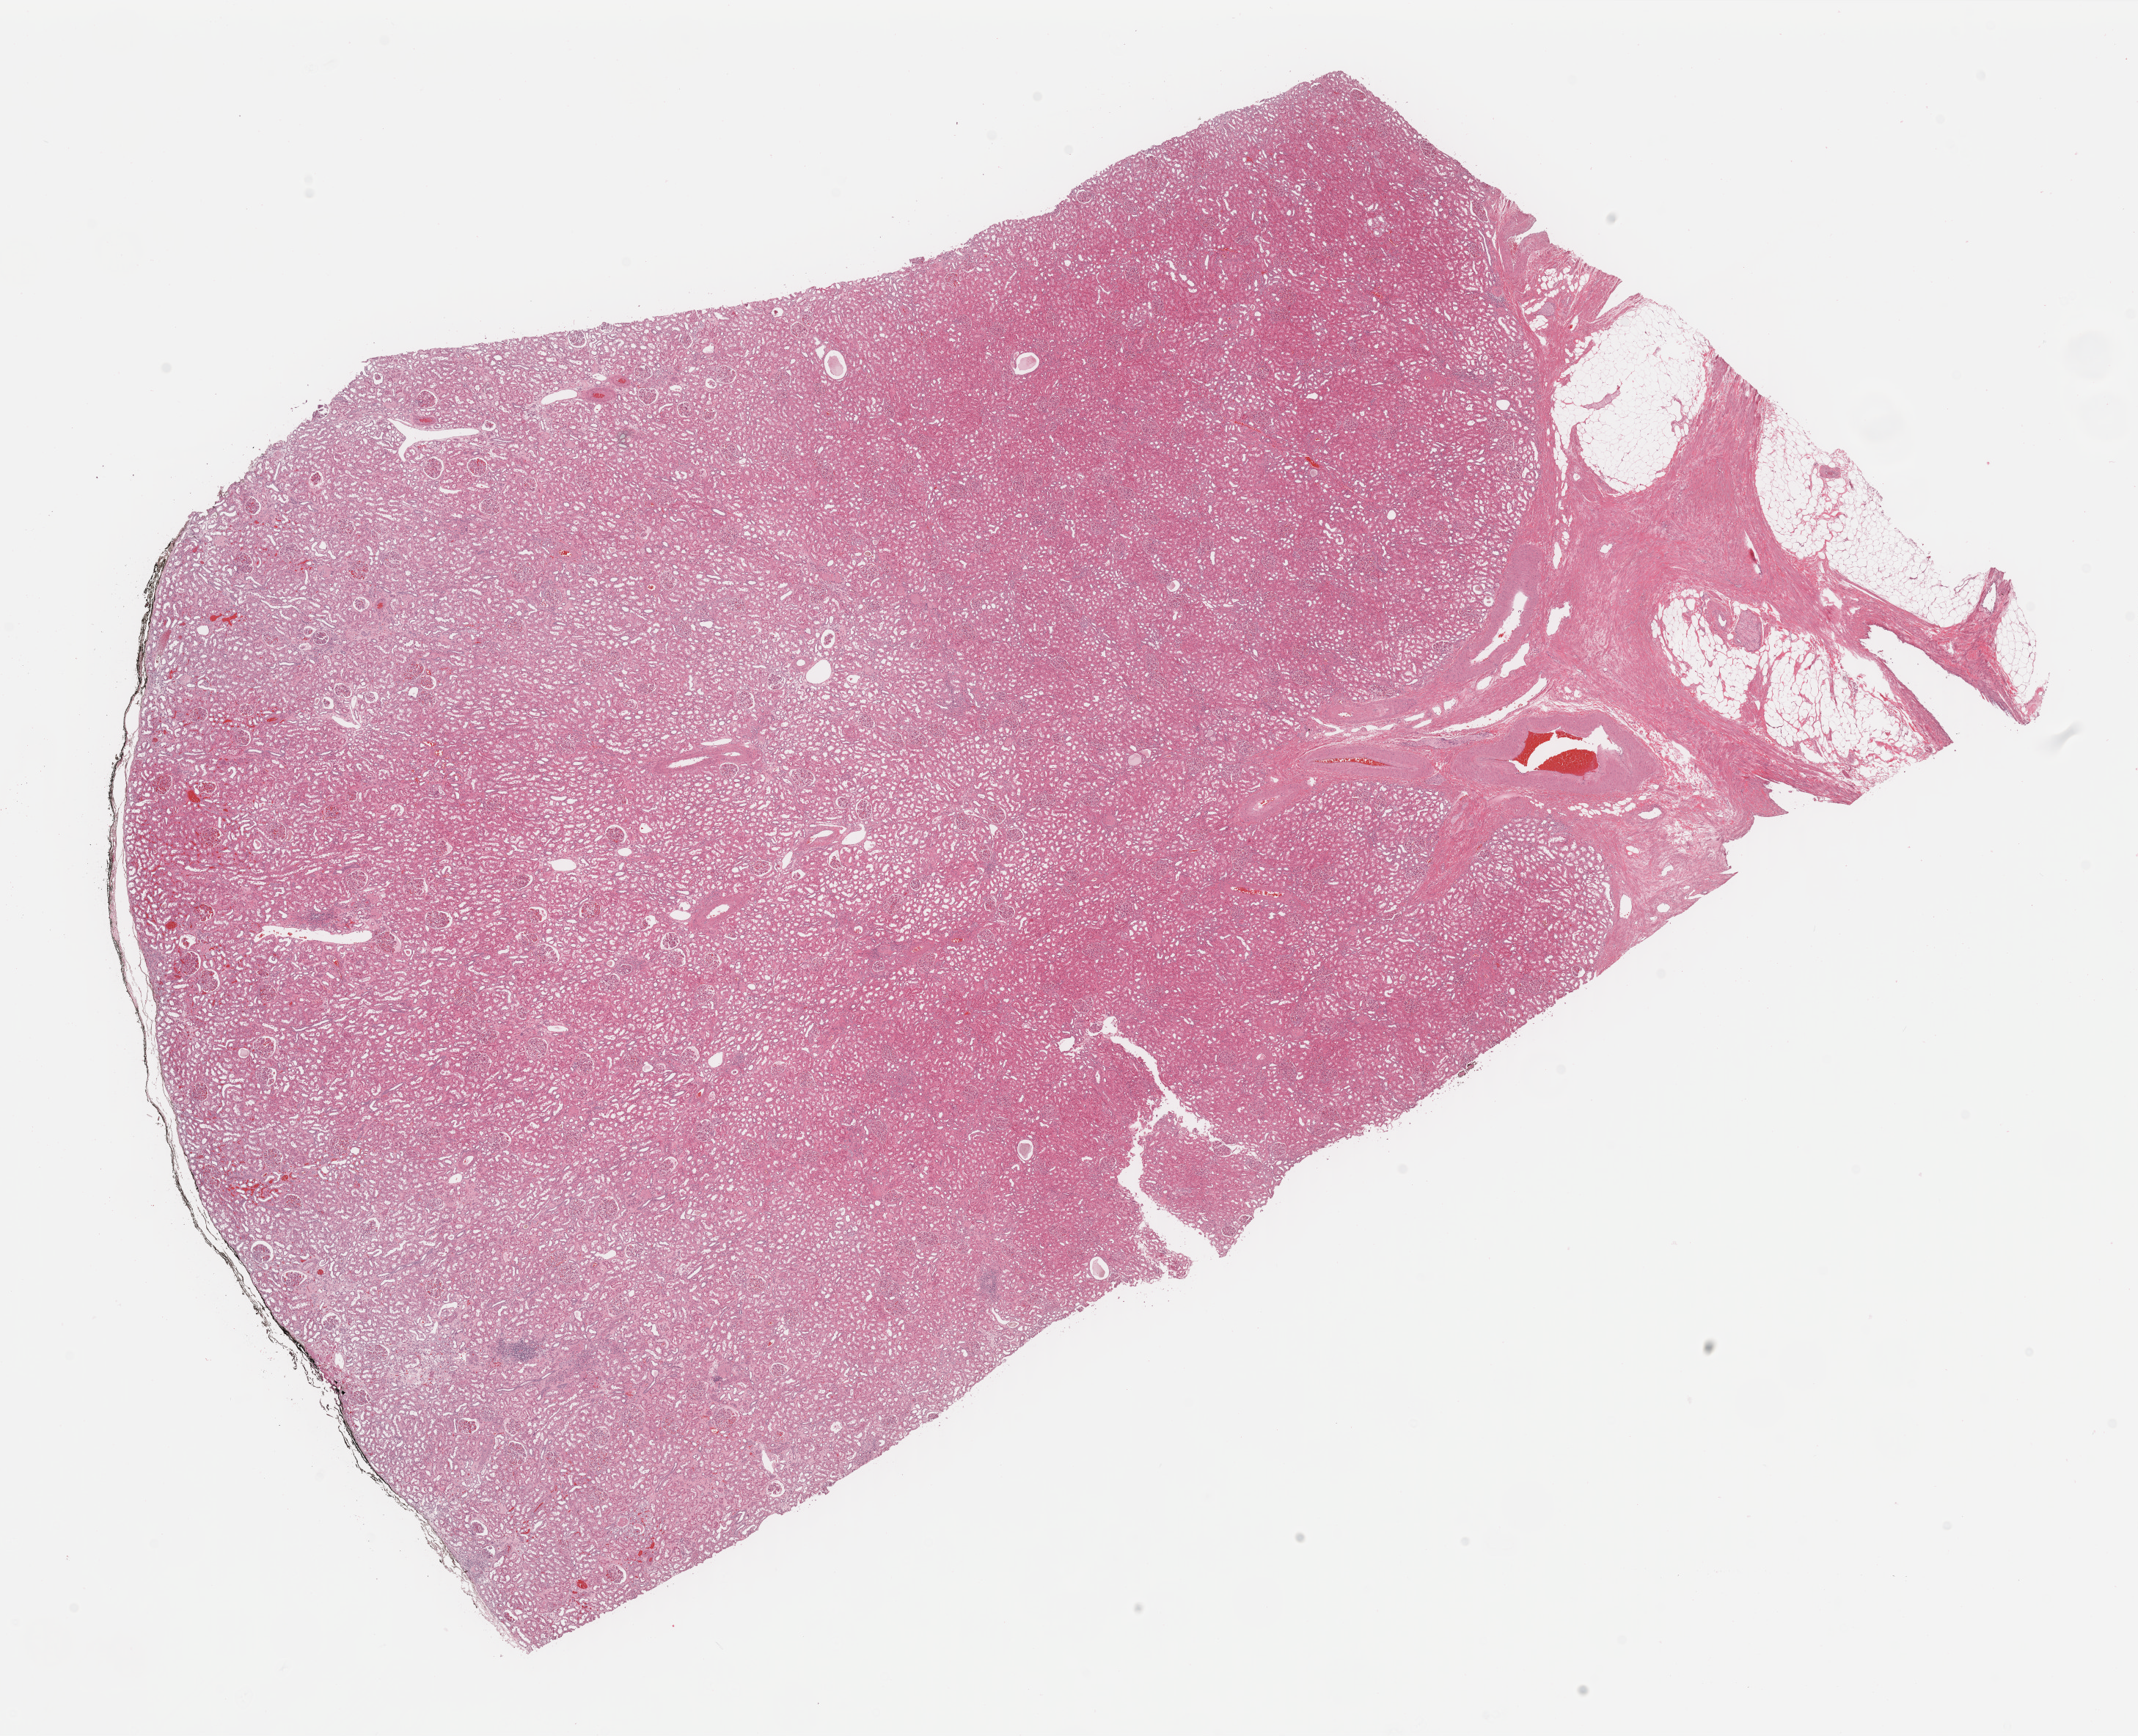
H&E-stained whole-slide image, whole scanned area (about 23.1 x 18.7 mm) shown as a low-resolution overview. Formalin-fixed paraffin-embedded (FFPE) diagnostic section. Kidney, solid tissue normal (non-tumour tissue) sample. Male, age 58 years at initial diagnosis. Slide review estimates, as recorded: tumour cells 0%, tumour nuclei 0%, normal cells 70%, stromal cells 30%, necrosis 0%. Infiltration values recorded for this section: lymphocyte infiltration 3%, monocyte infiltration 1%, neutrophil infiltration 1%.
This section: solid tissue normal (non-tumour) sample from the same patient. Patient diagnosis: Renal cell carcinoma, chromophobe type.